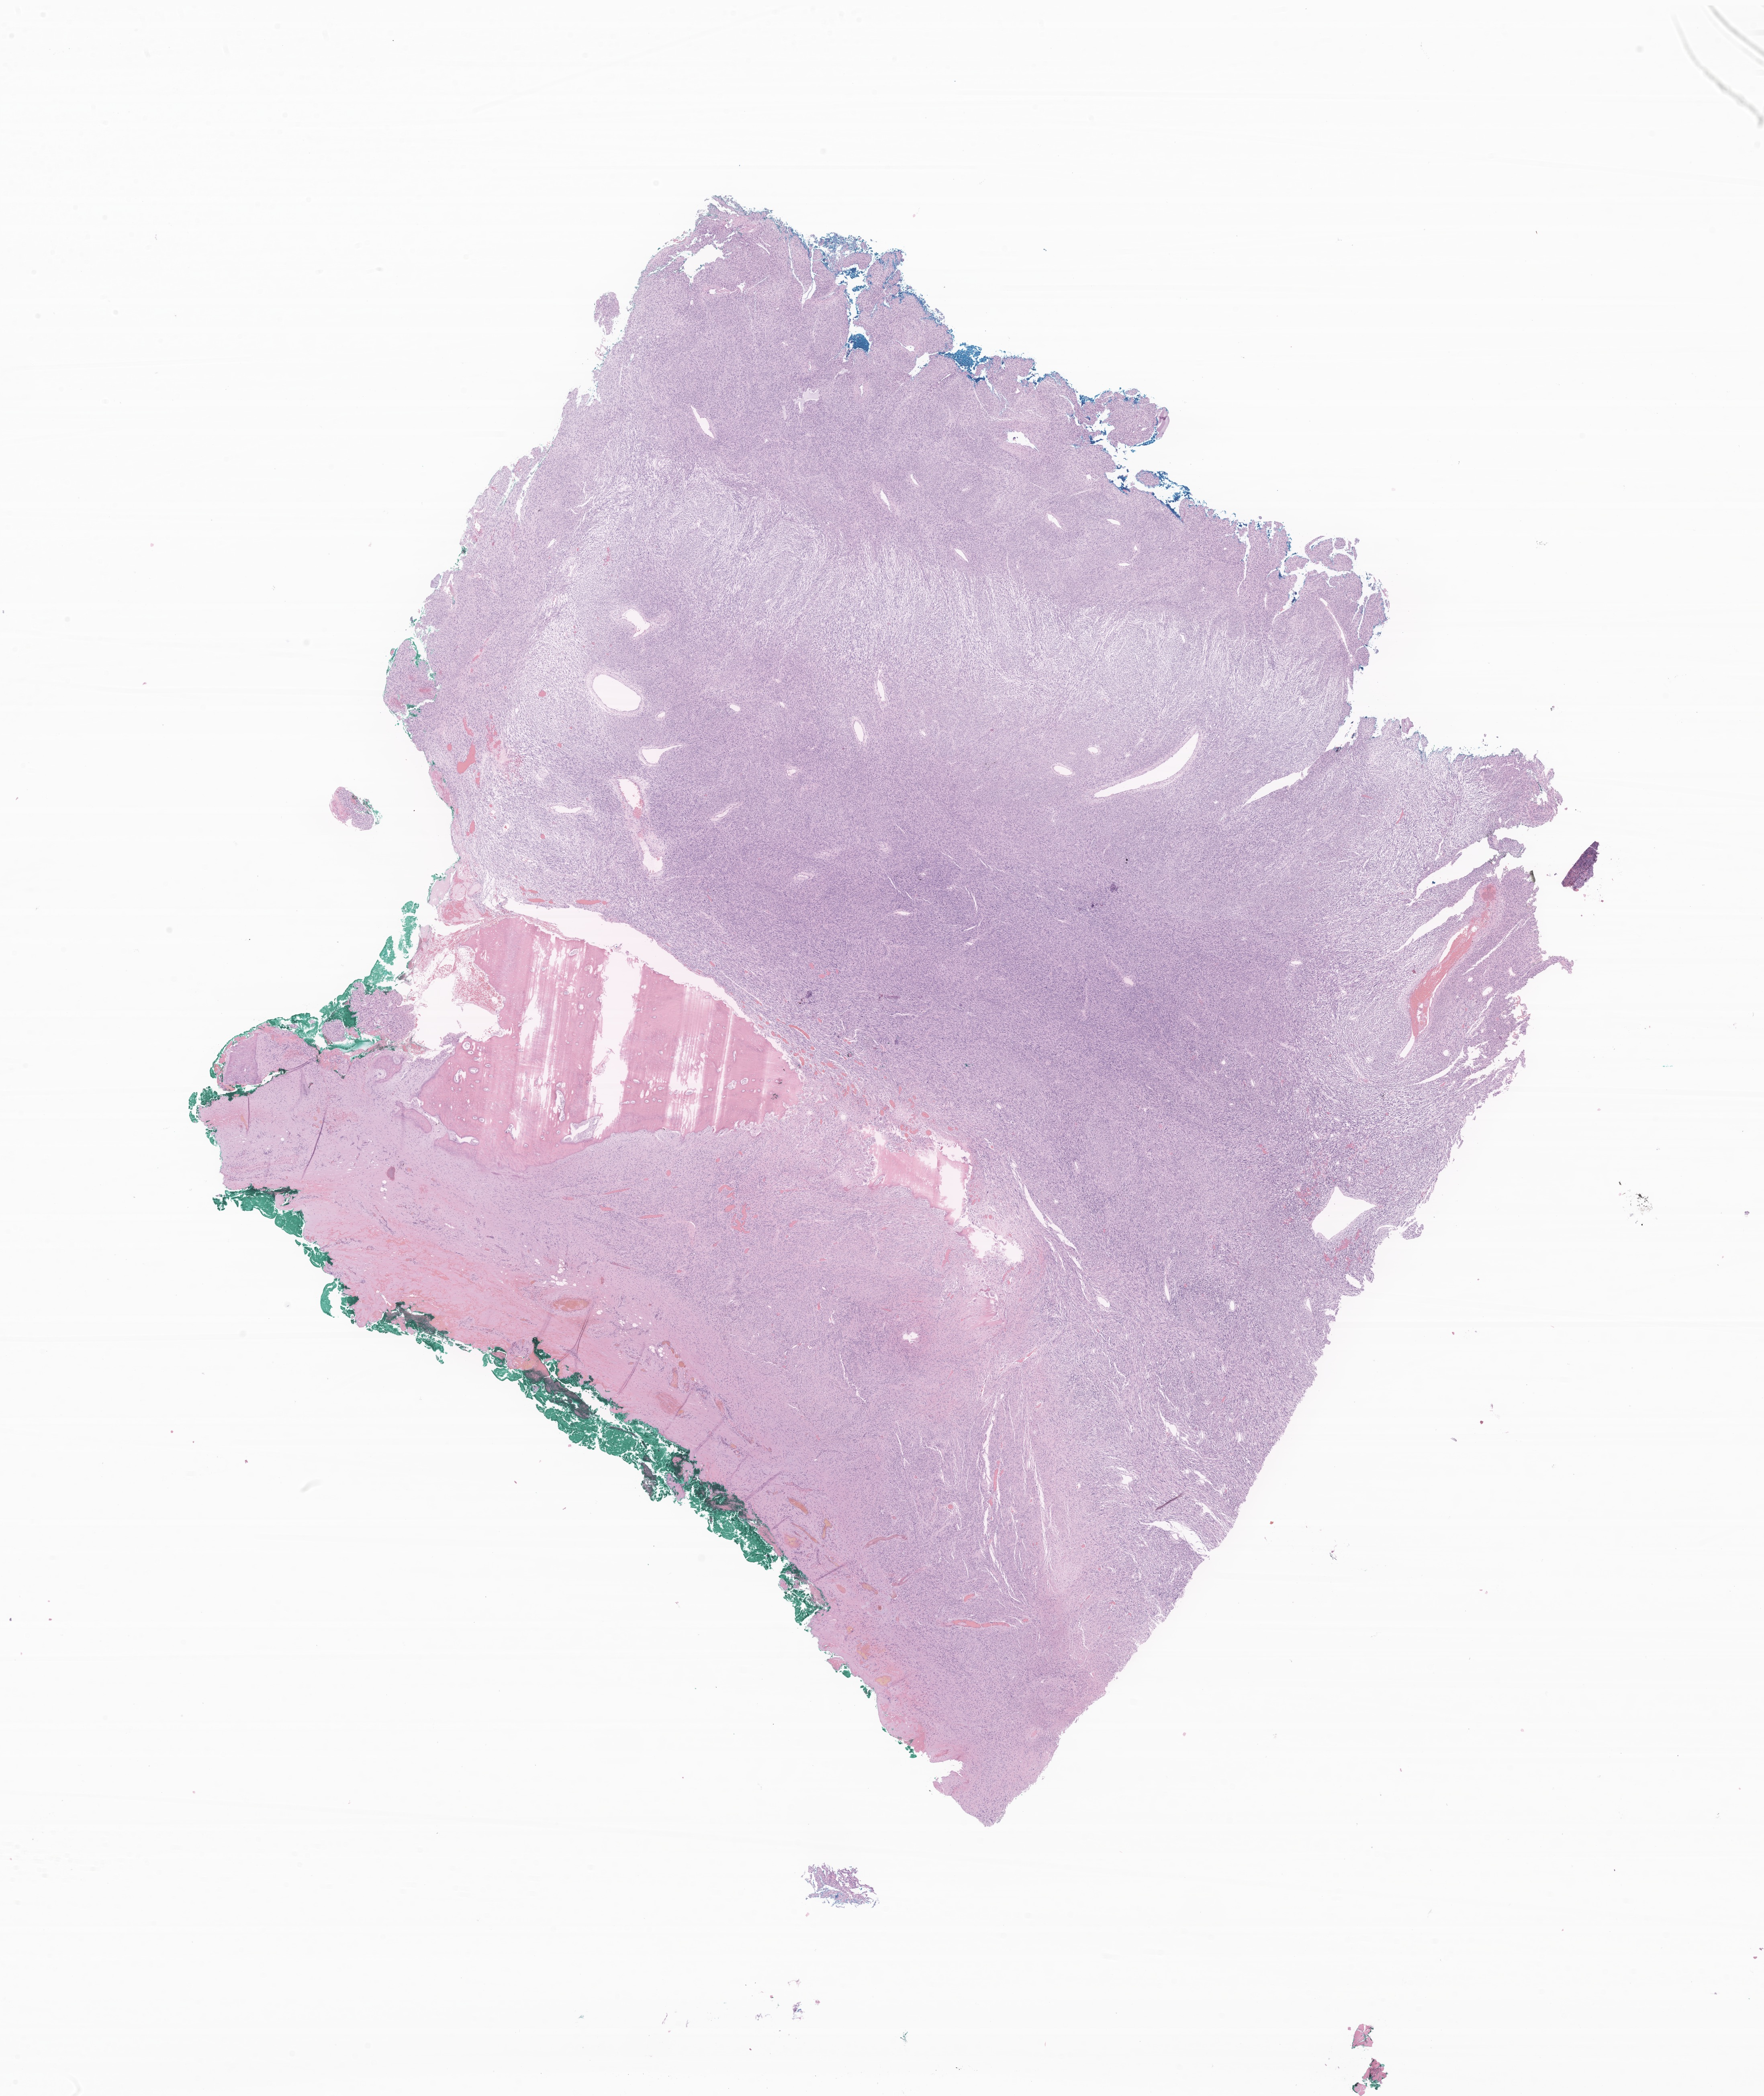
Whole-slide image, H&E stain of tumor tissue from the occipital lobe, shown as a low-resolution overview of the whole scanned area (about 18.5 x 22.0 mm); FFPE section. Patient: female, age 49 months (4 years 1 month).
Recorded diagnosis: Spindle cell sarcoma.